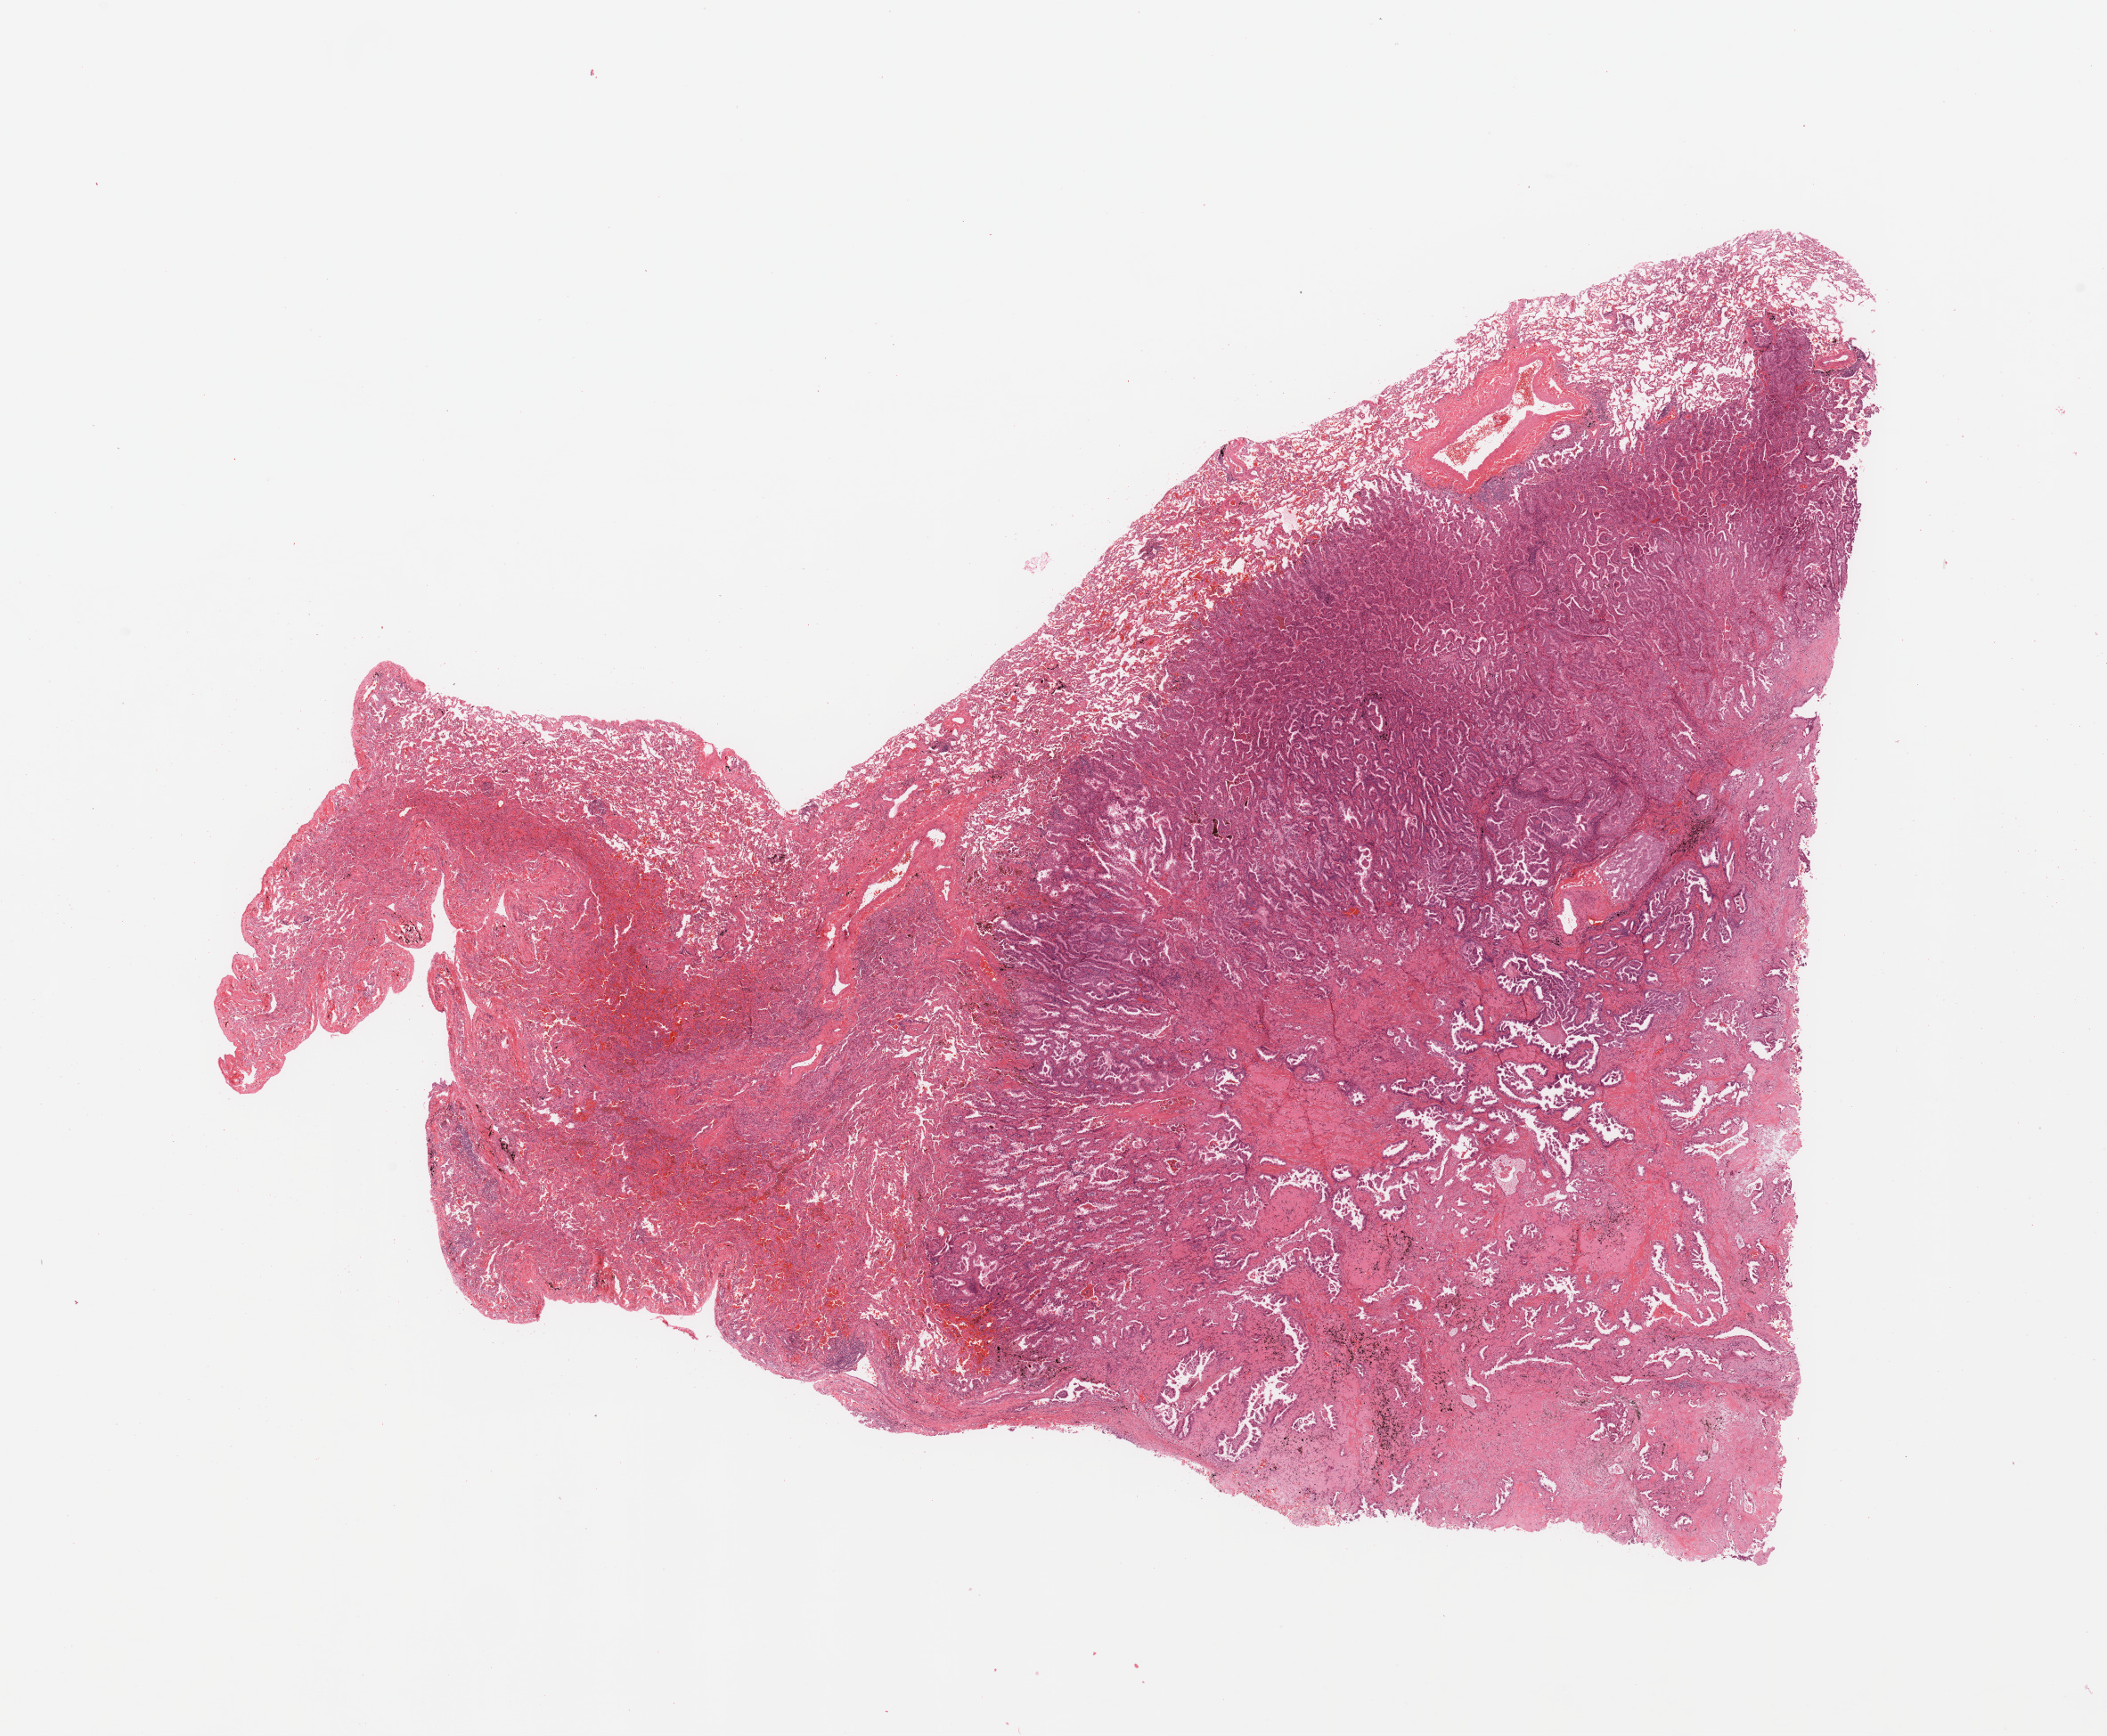
Digitized Hematoxylin and eosin (H&E) stained tissue section (whole slide), whole scanned area (about 18.7 x 15.4 mm, from a 20x scan) shown as a low-resolution overview; tumour tissue sample, sampled site: lung. 44-year-old female patient. Histologic grade: G2 (moderately differentiated). Pathologist review of this section (percent, as recorded): tumour nuclei 60%, necrosis 5%.
Diagnosis: Adenocarcinoma, NOS. AJCC pathologic stage: IIIA.